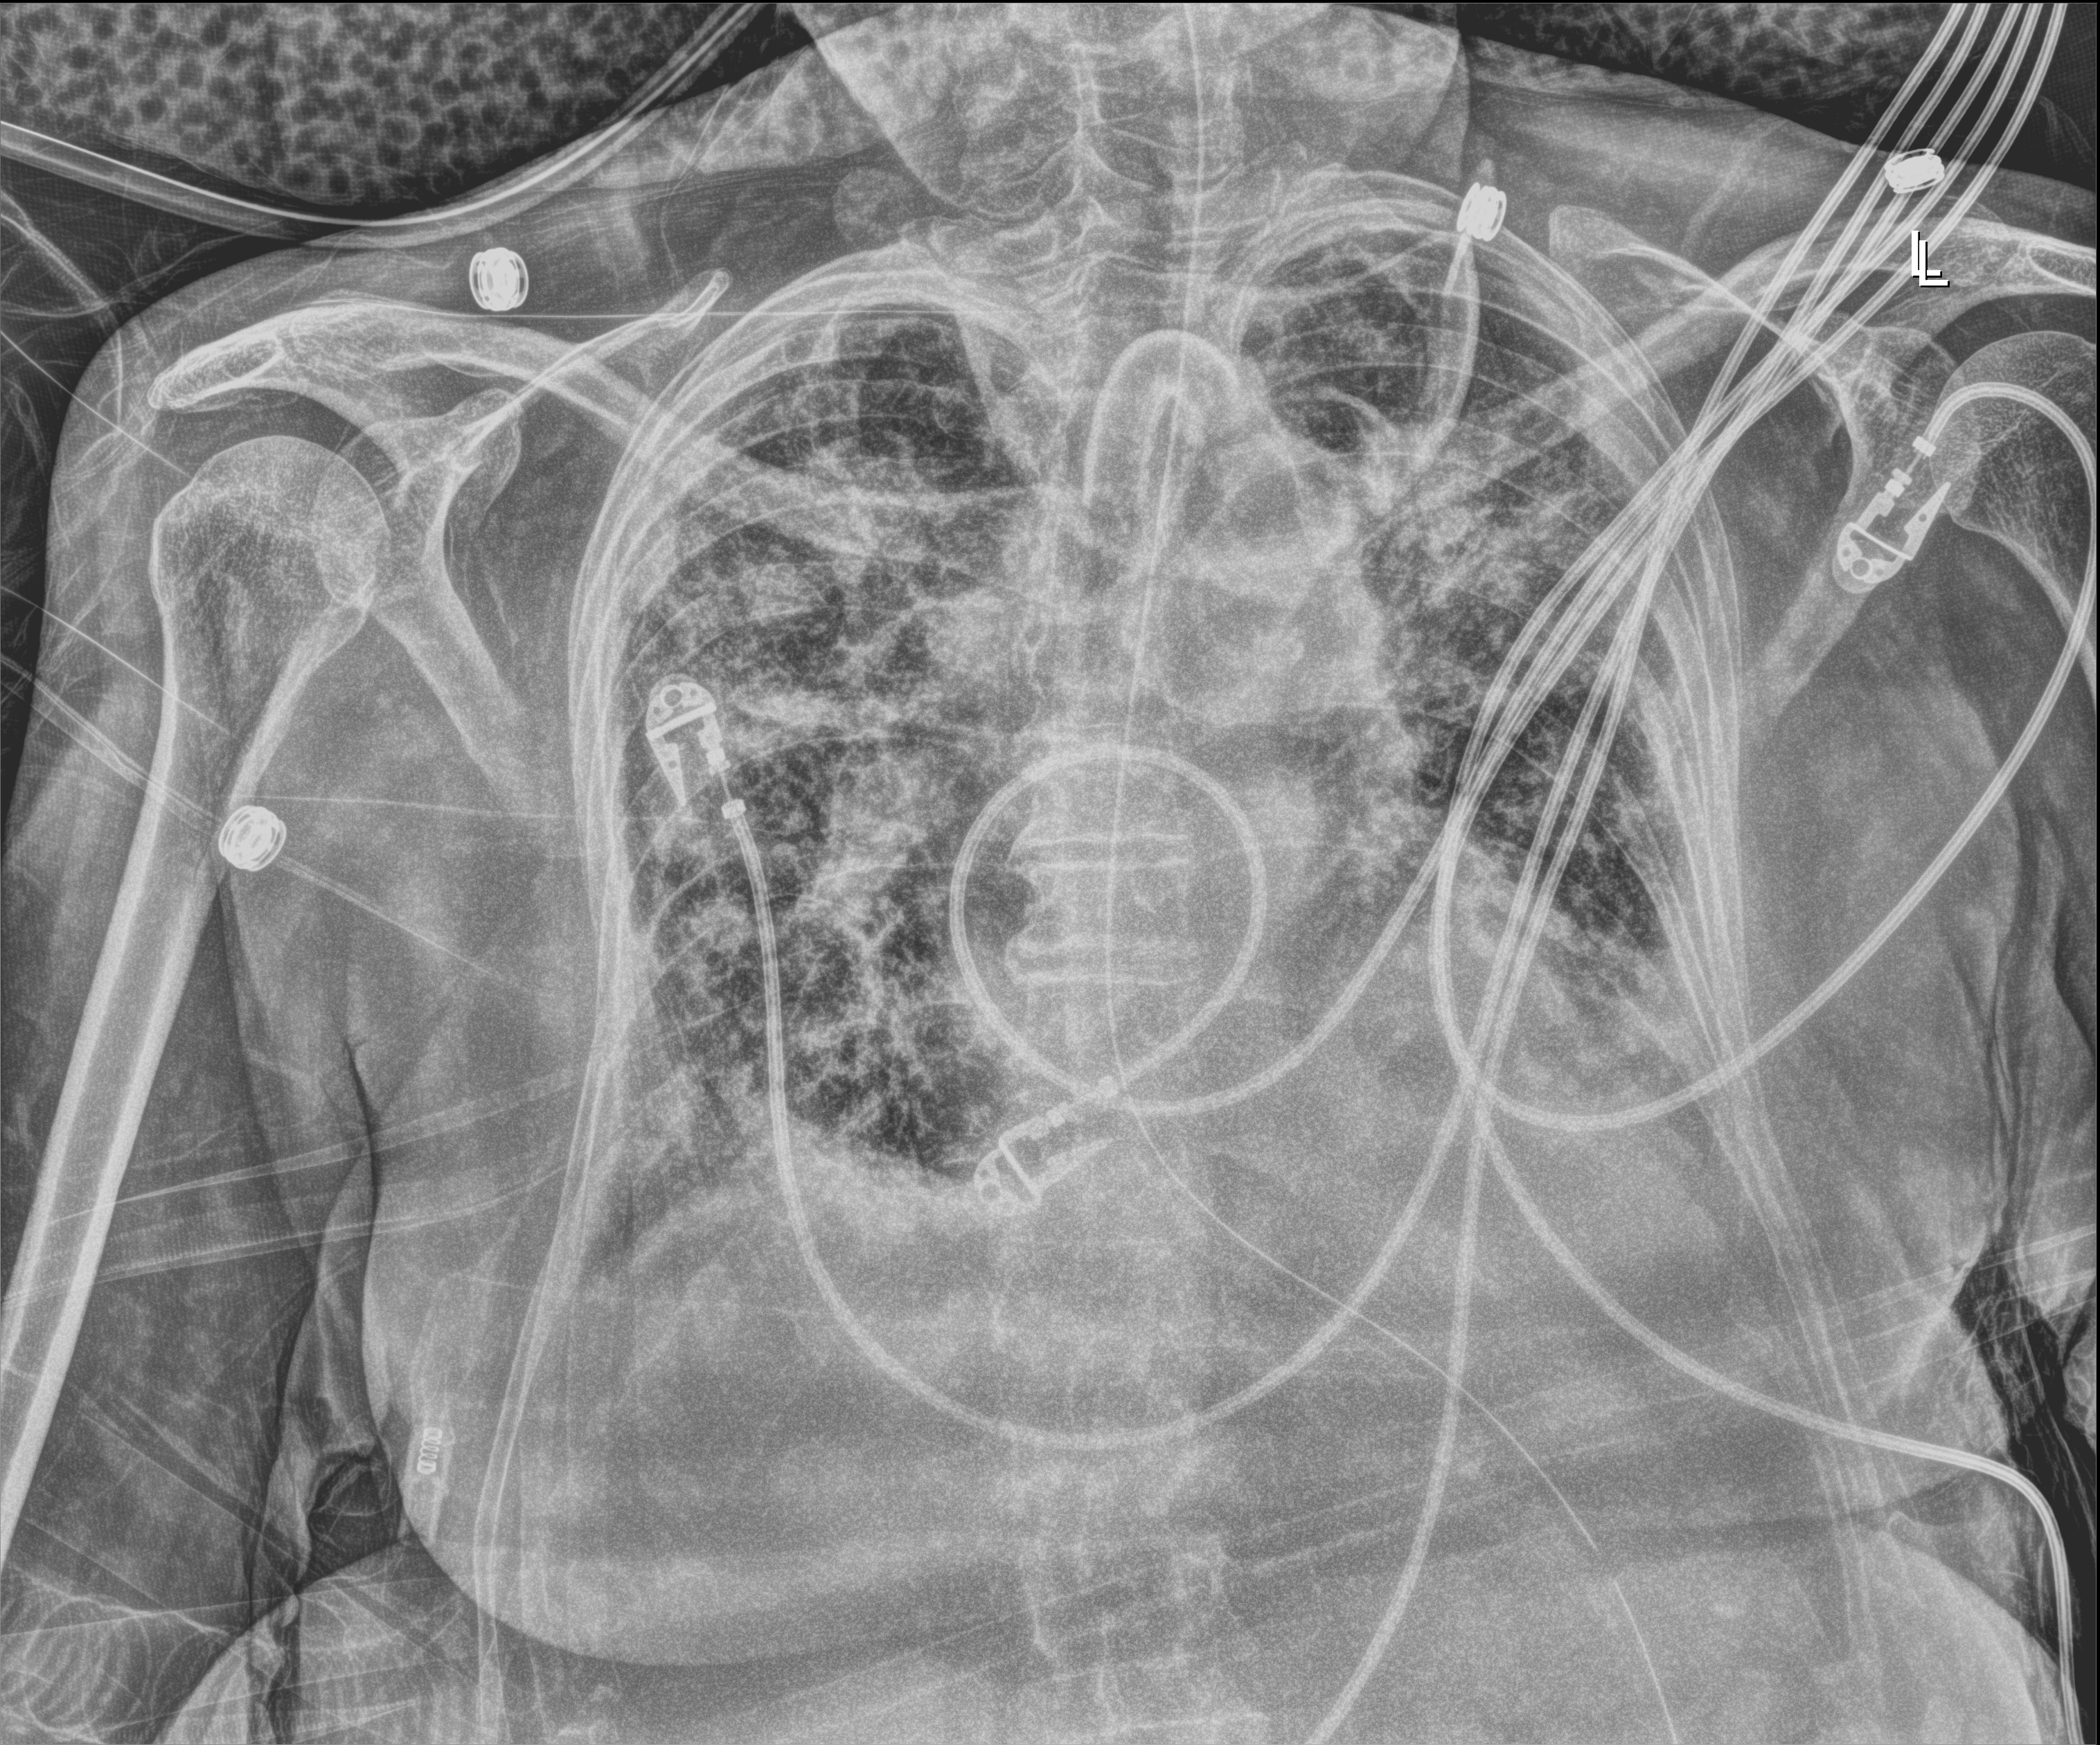
Chest X-ray (portable), anteroposterior (AP) projection. Female patient hospitalised with COVID-19, age 75–90 years.
Hospital-stay facts (about this admission, not read from this image; timing relative to this image not recorded): mechanically ventilated during this hospital stay: yes; admitted to intensive care during this hospital stay: yes.